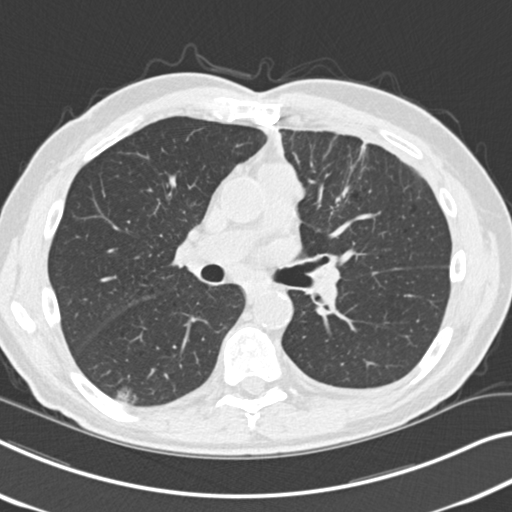
Axial slice from a low-dose chest CT screening exam; baseline annual screen; lung window (W 1500 / L -600 HU); standard (soft-tissue) reconstruction kernel (B30f); slice 101 of 212 in the series; 512 × 512 image matrix. Male, age 68 years at enrolment. Current smoker at enrolment.
Lesion marked by an expert reader, bounding box [x1, y1, x2, y2] px = [97, 379, 148, 415]. Screening reader's record for this exam (one nodule recorded; not confirmed to be the boxed lesion): non-calcified nodule or mass ≥4 mm, right lower lobe, 14 × 10 mm, poorly defined margins, ground glass attenuation. Participant outcome: lung cancer diagnosed 1018 days after this screen — non-small cell carcinoma, right lower lobe, poorly differentiated (G3), stage IA (AJCC 6th edition), 23 mm at pathology.